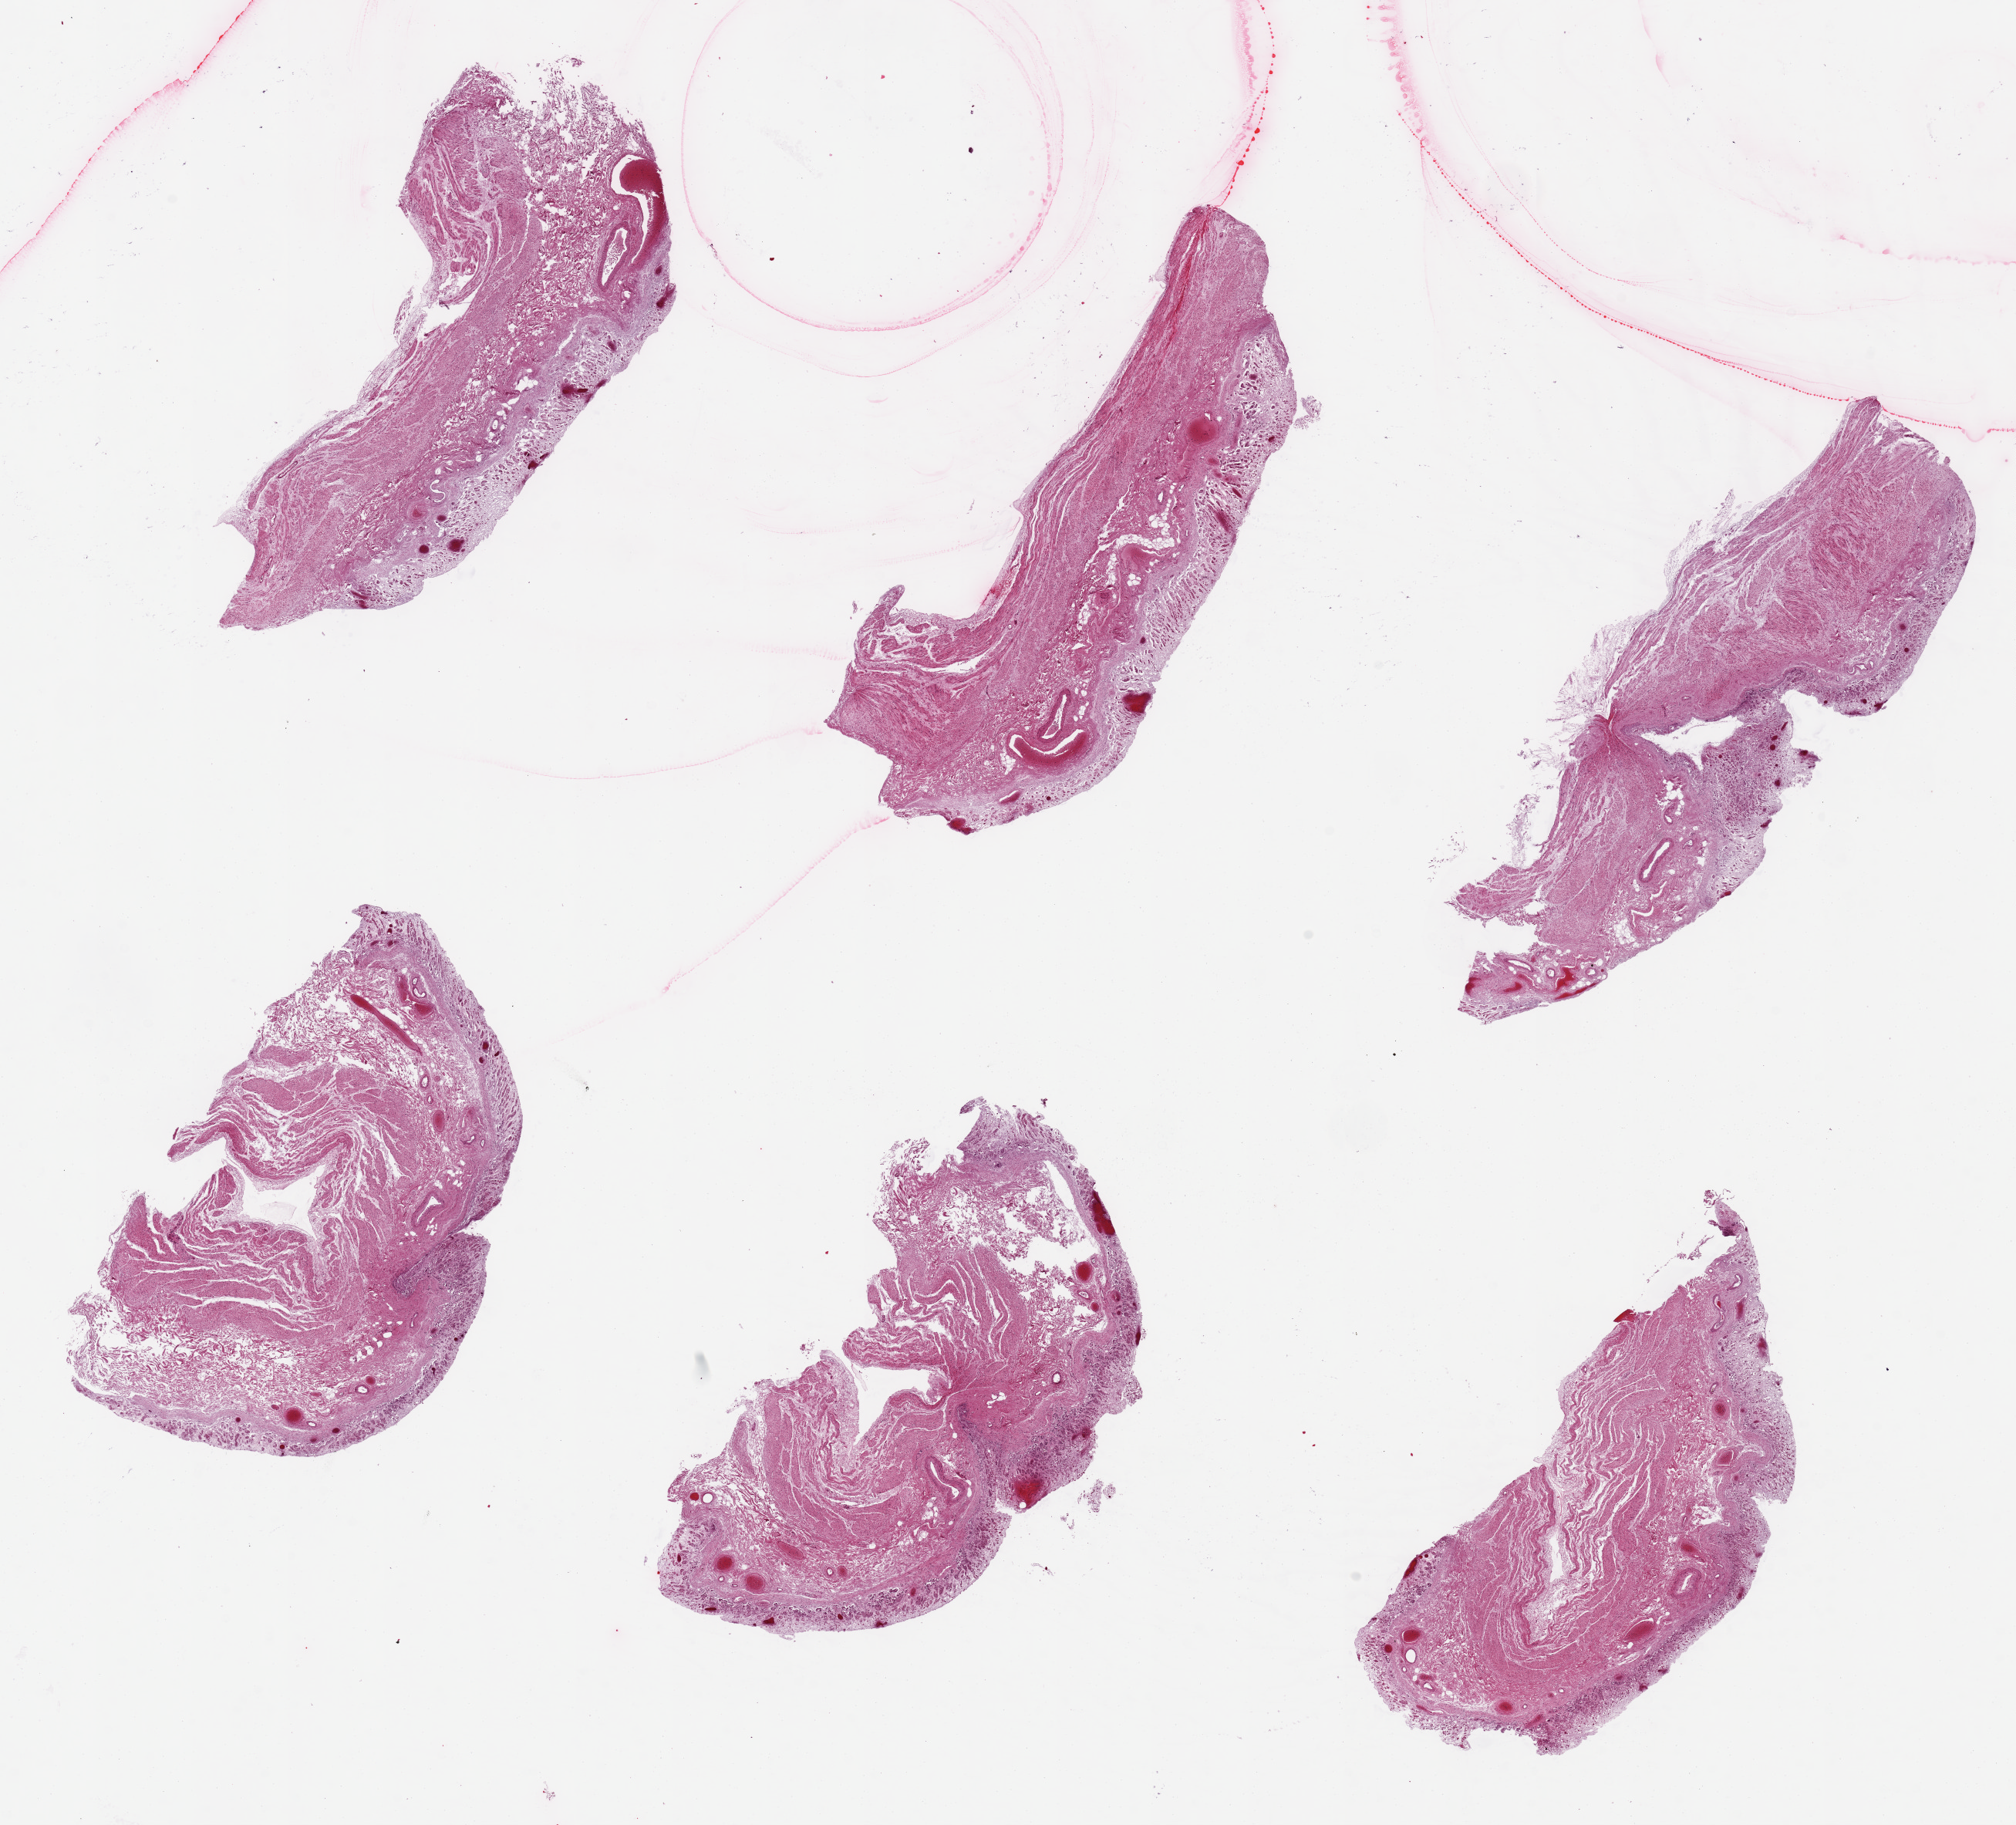
H&E whole-slide image, shown as a low-resolution overview of the whole scanned area (about 20.7 x 18.7 mm). PAXgene-fixed paraffin-embedded (PFPE) section. Sampled site (target tissue): stomach. Donor tissue sample. Donor sex: female.
Pathologist's review note for this sample: 6 pieces up to 7x3 mm; mucosa totally autolyzed; wall moderately autolyzed.